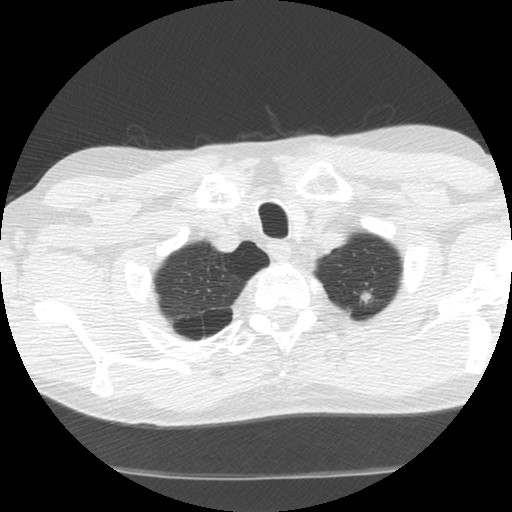
Chest CT (low-dose screening protocol), one axial image; first (baseline) screen; lung window (W 1500 / L -600 HU); 2.5 mm slice thickness; standard (soft-tissue) reconstruction kernel (STANDARD); slice 117 of 130 in the series; 512 × 512 image matrix. Male participant, aged 63 years at enrolment.
- Expert reader's lesion annotation, bounding box [x1, y1, x2, y2] px = [338, 278, 389, 328].
- The screening reader recorded 4 non-calcified nodules or masses ≥4 mm on this exam (left upper lobe, right upper lobe, right lower lobe, right lower lobe); which of them this box marks is not recorded.
- Lung cancer was diagnosed 629 days after this screen (after the second annual screen): adenocarcinoma, NOS, left upper lobe, moderately differentiated (G2), stage IB (AJCC 6th edition), 14 mm at pathology.